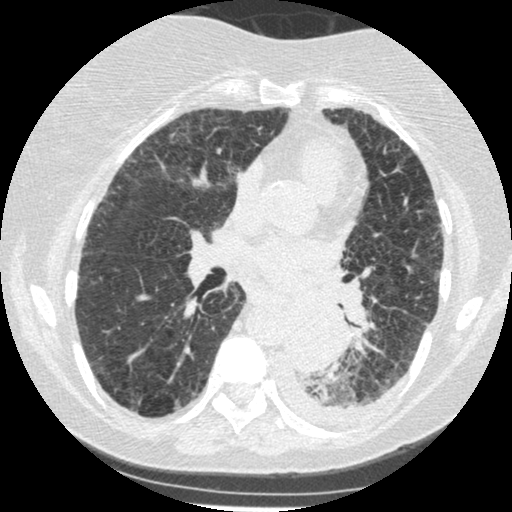
Low-dose screening chest CT, one axial slice. Reconstruction kernel STANDARD. Lung window (W 1500 / L -600 HU). 512 × 512 image matrix, field of view 310 × 310 mm.
Structures marked on this image (outlined manually by an expert reader):
- lesion 1 (tumor, lower lobe of left lung): bounding box [x1, y1, x2, y2] px = [284, 302, 346, 375]